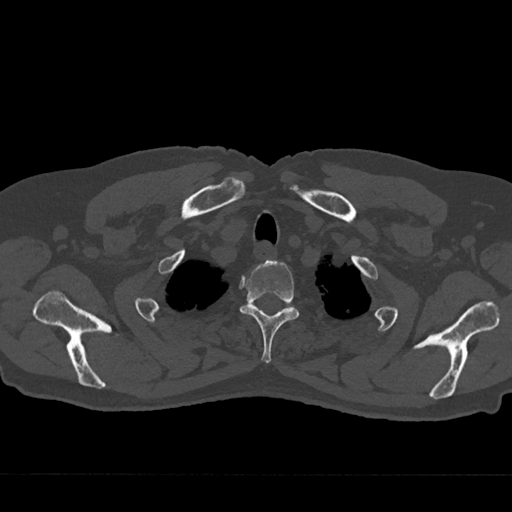
CT including the spine, one axial slice; slice 611 of 797 in the series (ordered by position); reconstruction kernel Br40s/3; bone window (W 1800 / L 400 HU); 512 × 512 image matrix, field of view 377 × 377 mm. Male patient, age 75 years. From the clinical record (not read from this slice): primary cancer: renal; vertebrae with lytic lesions (as recorded): T4.
Structures marked on this image (semi-automatic segmentation, software-assisted and operator-edited):
- T2 vertebra: box from (x=240, y=260) to (x=299, y=363) px